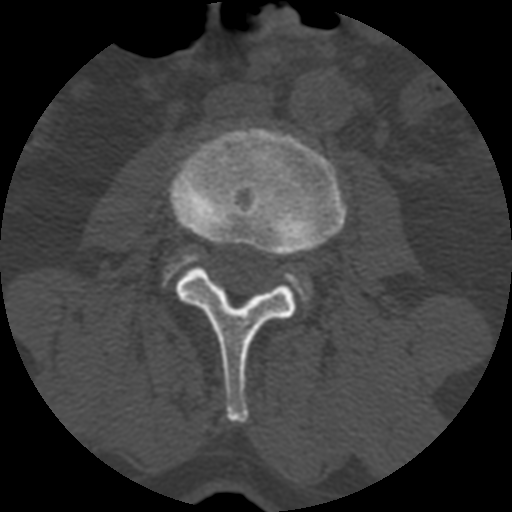
CT including the spine, one axial slice. Position 300 of 399 along the scan axis. Reconstruction kernel STANDARD. 120 kVp. Bone window (W 1800 / L 400 HU). 1.25 mm slice thickness. 512 × 512 image matrix, field of view 160 × 160 mm. Patient age 71 years. From the clinical record (not read from this slice): primary cancer: prostate.
Annotated regions visible in this slice (semi-automatically segmented with operator editing):
- L3 vertebra: box from (x=170, y=128) to (x=346, y=422) px
- L4 vertebra: (x=161, y=251)–(x=311, y=307)